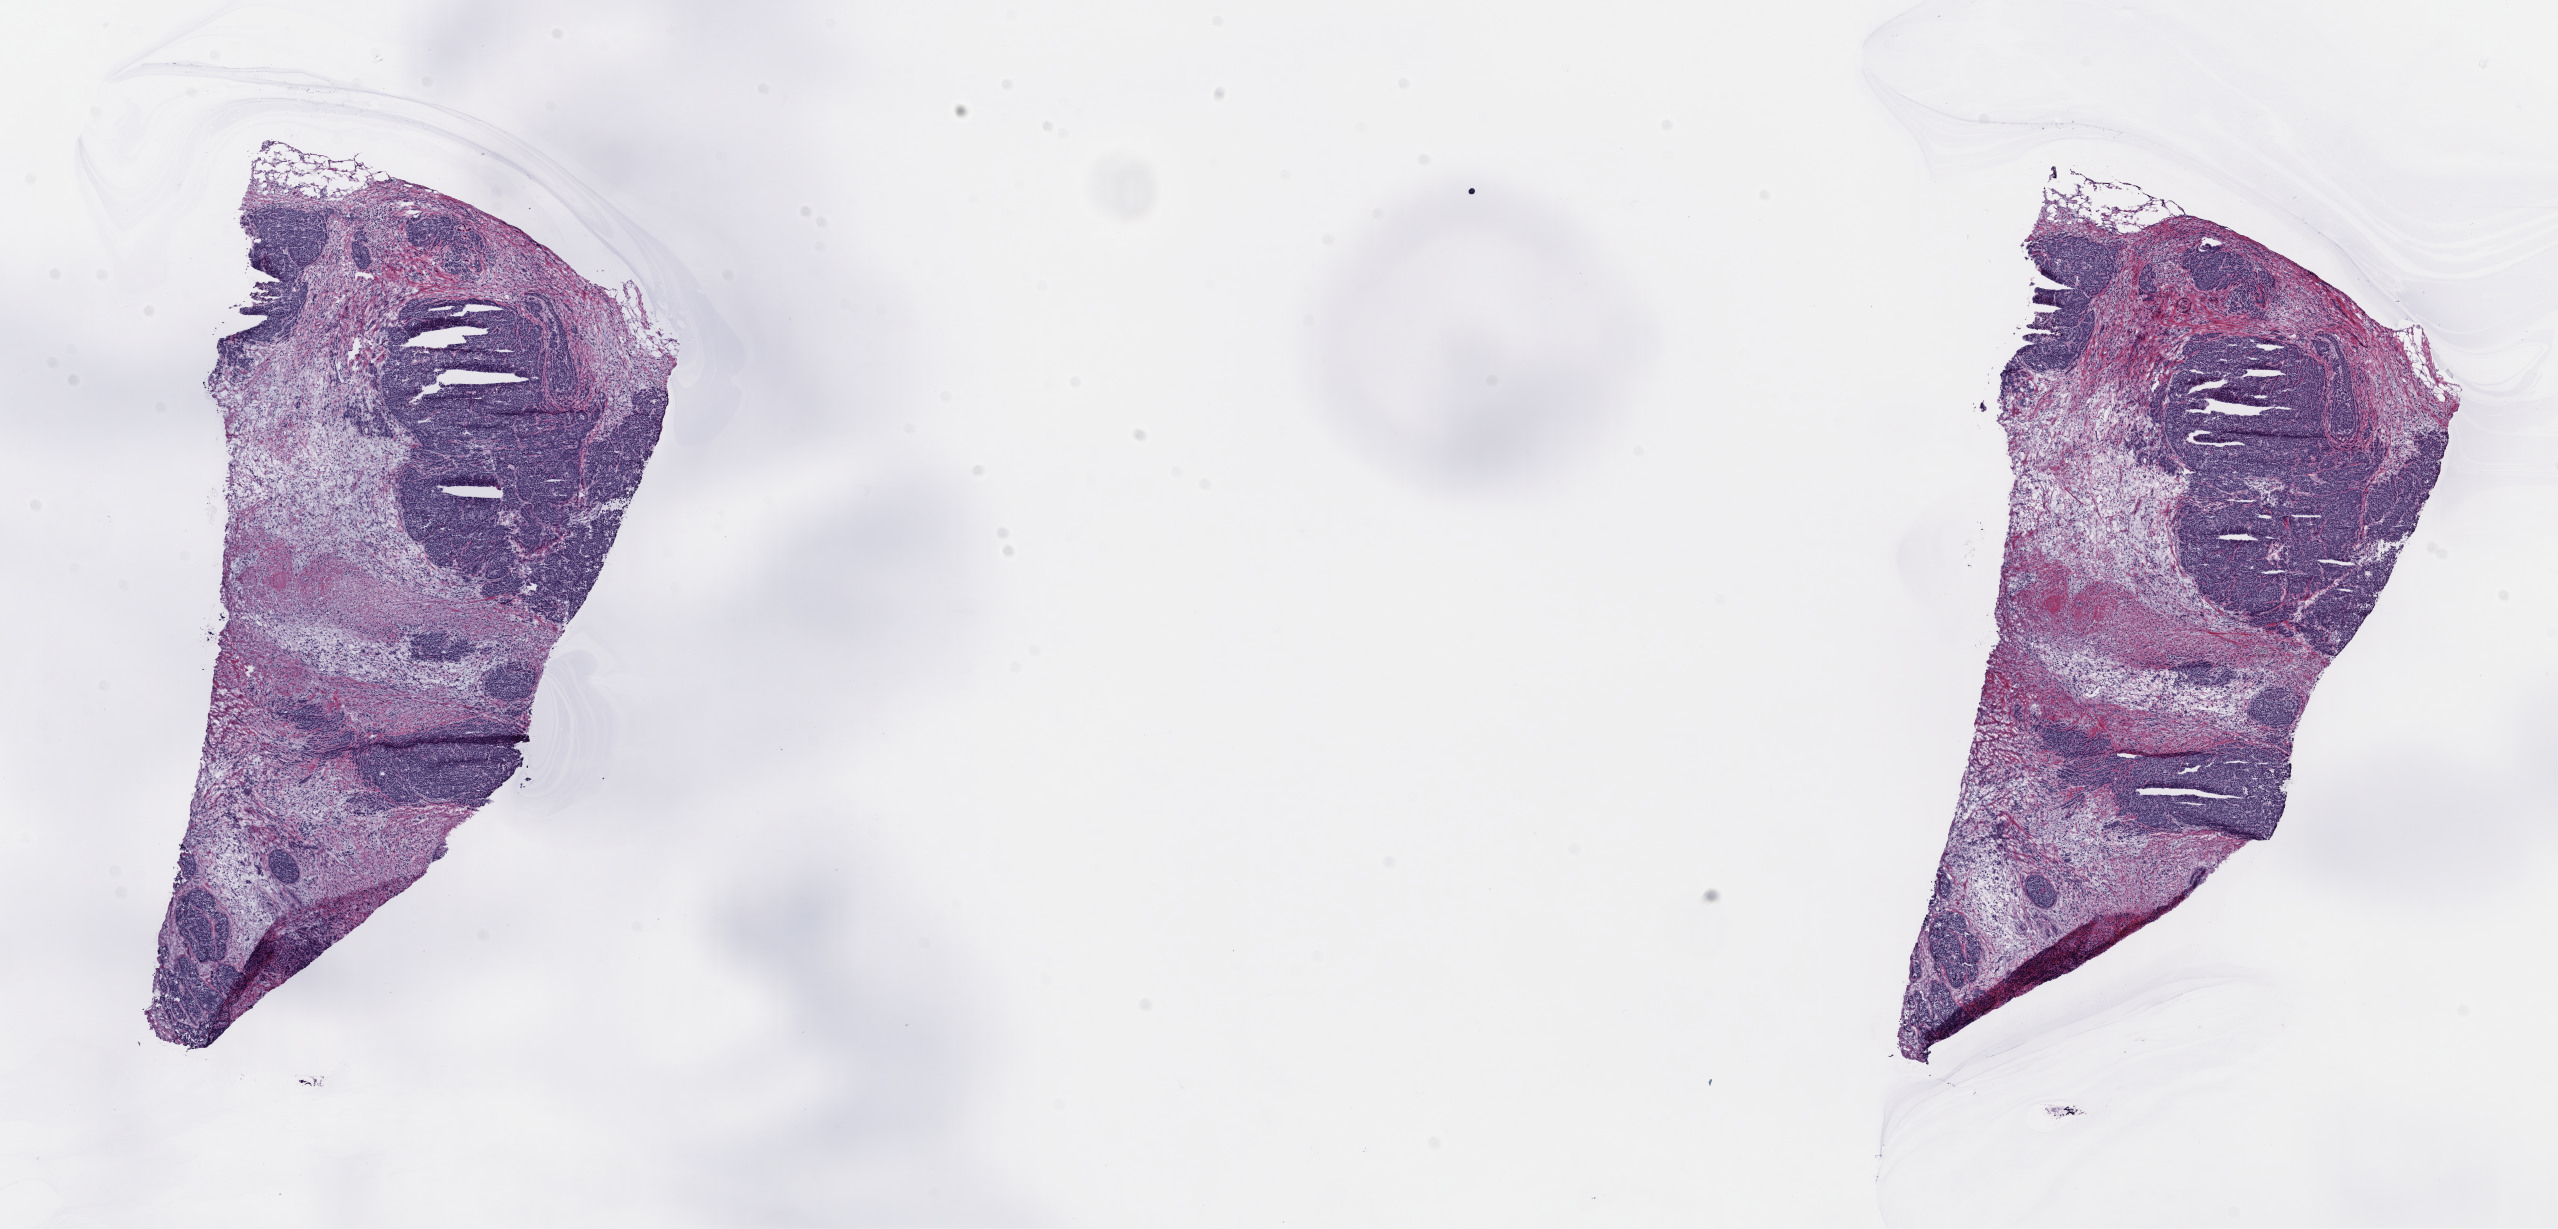
Whole-slide histology image, H&E-stained — whole scanned area (about 20.1 x 9.7 mm) shown as a low-resolution overview, frozen section, primary tumour sample from the breast. Female patient; age at initial diagnosis 45 years. Composition of this section per pathologist review: tumour cells 100%, tumour nuclei 85%, normal cells 0%, stromal cells 0%, necrosis 0%. Infiltration values recorded for this section: lymphocyte infiltration 0%, monocyte infiltration 0%, neutrophil infiltration 0%.
• AJCC pathologic stage: IIA (7th edition)
• laterality: left
• histologic diagnosis: Infiltrating duct carcinoma, NOS